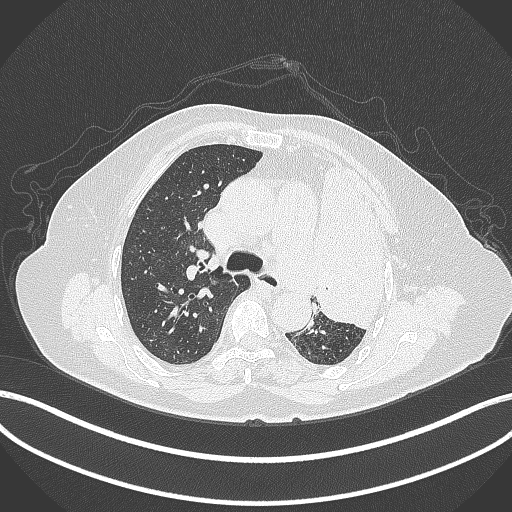
Chest CT, one axial slice; slice 258 of 399 in the series (ordered by position); reconstruction kernel B70f; lung window (W 1500 / L -600 HU); 512 × 512 image matrix, field of view 400 × 400 mm. Patient: female, 75 years. From the clinical record (not read from this slice): clinical TNM (as recorded): T3 N3 M1.
Outlined on this slice (rectangle marked by the reading radiologist):
- lung tumour (recorded histology: adenocarcinoma): bounding box <314,153,386,332> (left, top, right, bottom; pixels)